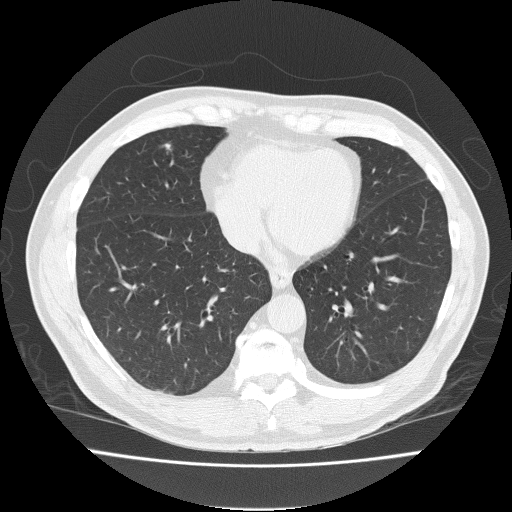
Chest CT (low-dose screening protocol), one axial image, first (baseline) screen, lung window (W 1500 / L -600 HU), 2 mm slice thickness, 512 × 512 image matrix. Male participant, aged 57 years at enrolment. Current smoker at enrolment.
• Lesion marked by an expert reader, bounding box (x1, y1, x2, y2) in pixels: (151, 134, 184, 162).
• Reader record for this screening exam (exam-level; its link to the box is not recorded): non-calcified nodule or mass ≥4 mm, right middle lobe, 4 × 4 mm, spiculated (stellate) margins, soft tissue attenuation.
• Later outcome: lung cancer diagnosed 459 days after this screen (after the second annual screen) — adenocarcinoma, NOS, right middle lobe, moderately differentiated (G2), stage IA (AJCC 6th edition), 12 mm at pathology.